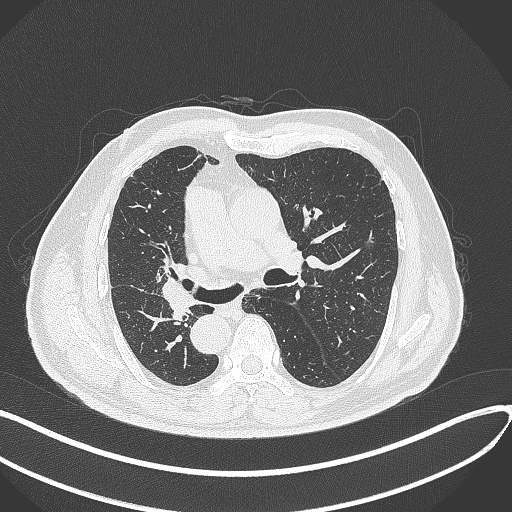
Chest CT, one axial slice; position 170 of 300 along the scan axis; reconstruction kernel B70f; 120 kVp; lung window (W 1500 / L -600 HU); 1 mm slice thickness; 512 × 512 image matrix, field of view 400 × 400 mm. Patient: male, 67 years. From the clinical record (not read from this slice): clinical TNM (as recorded): T2a N0 M0.
Outlined on this slice (bounding box drawn by a radiologist):
- lung tumour (recorded histology: squamous cell carcinoma): box from (x=156, y=275) to (x=201, y=325) px